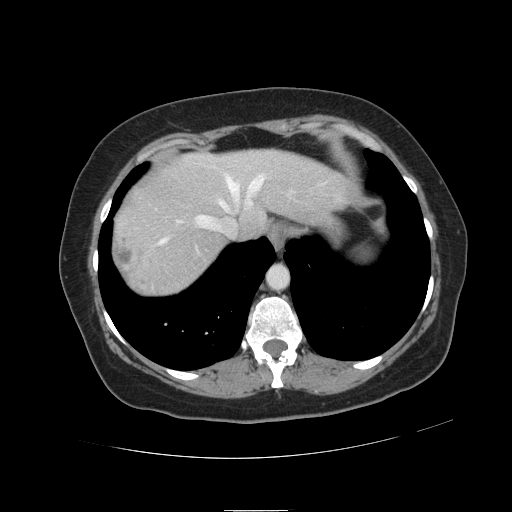
Contrast-enhanced abdominal CT, one axial slice; slice 101 of 121 in the series (ordered by position); intravenous contrast given; soft-tissue window (W 400 / L 40 HU); 2.5 mm slice thickness; 512 × 512 image matrix. Female patient, age 52 years. From the clinical record (not read from this slice): diagnosis: colorectal cancer liver metastases, imaged before liver resection; multiple liver metastases: yes; largest metastasis: 6.3 cm.
Annotated regions visible in this slice (outlined manually by an expert reader):
- hepatic veins: bounding box <159,175,293,252> (left, top, right, bottom; pixels)
- liver: <113,150,348,296>
- planned liver remnant (the part of the liver to remain after resection): <174,150,347,238>
- liver metastasis: <116,247,133,275>